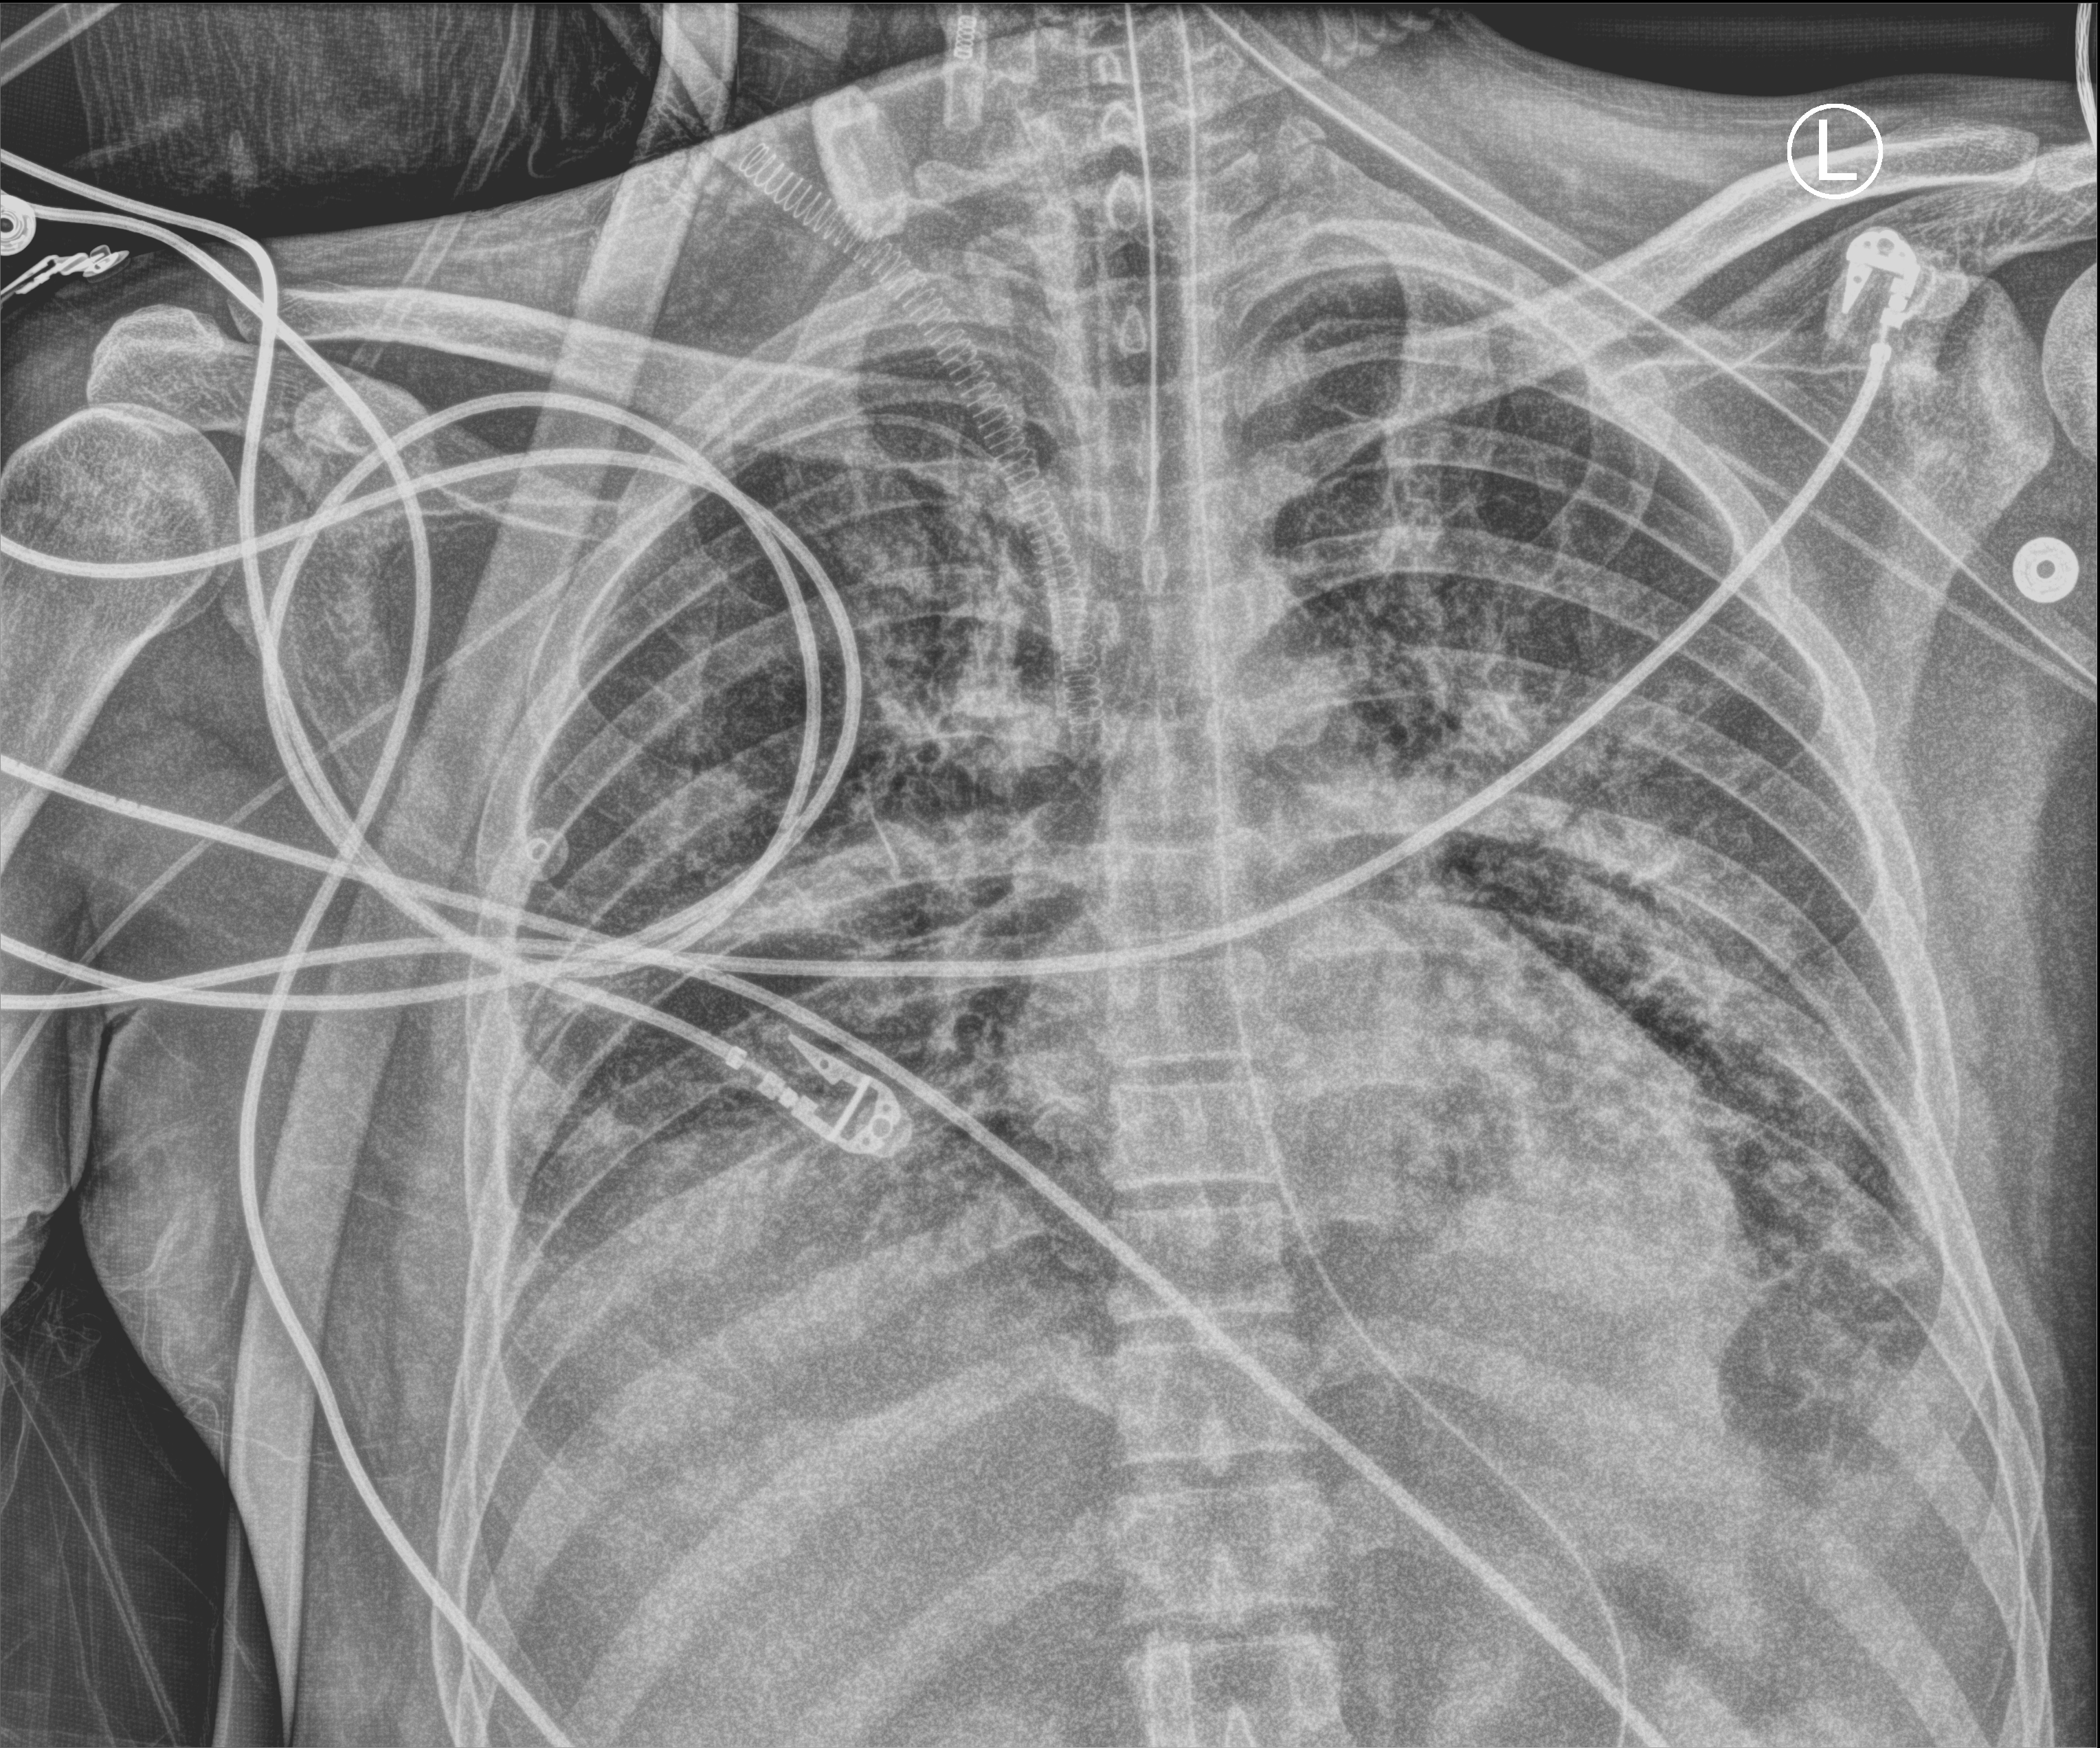
Portable chest radiograph; anteroposterior (AP) projection. Adult patient hospitalised with COVID-19, age 18–59 years.
Hospital-stay facts (about this admission, not read from this image; timing relative to this image not recorded): diabetes (admission record): no; admitted to intensive care during this hospital stay: yes; mechanically ventilated during this hospital stay: yes.